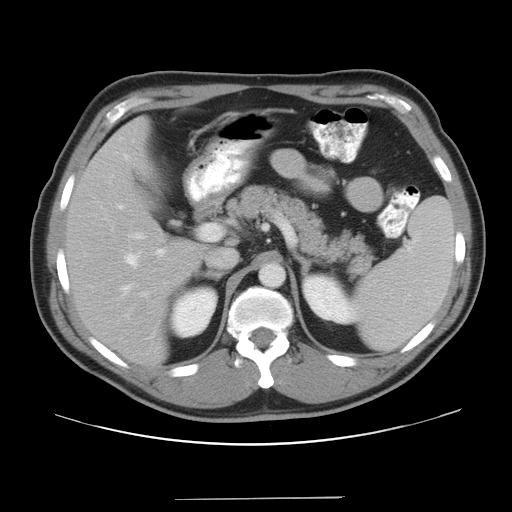
Contrast-enhanced abdominal CT, one axial slice; slice 24 of 37 in the series (ordered by position); reconstruction kernel STANDARD; intravenous contrast given; soft-tissue window (W 400 / L 40 HU); 512 × 512 image matrix, field of view 400 × 400 mm. Male patient, age 46 years. From the clinical record (not read from this slice): diagnosis: colorectal cancer liver metastases, imaged before liver resection; multiple liver metastases: yes; largest metastasis: 1 cm; disease in both lobes: no.
Outlined on this slice (outlined manually by an expert reader):
- hepatic veins: bounding box <122,253,139,293> (left, top, right, bottom; pixels)
- liver: <68,120,202,360>
- planned liver remnant (the part of the liver to remain after resection): <68,120,202,360>
- portal vein (with intrahepatic branches): <137,234,165,254>